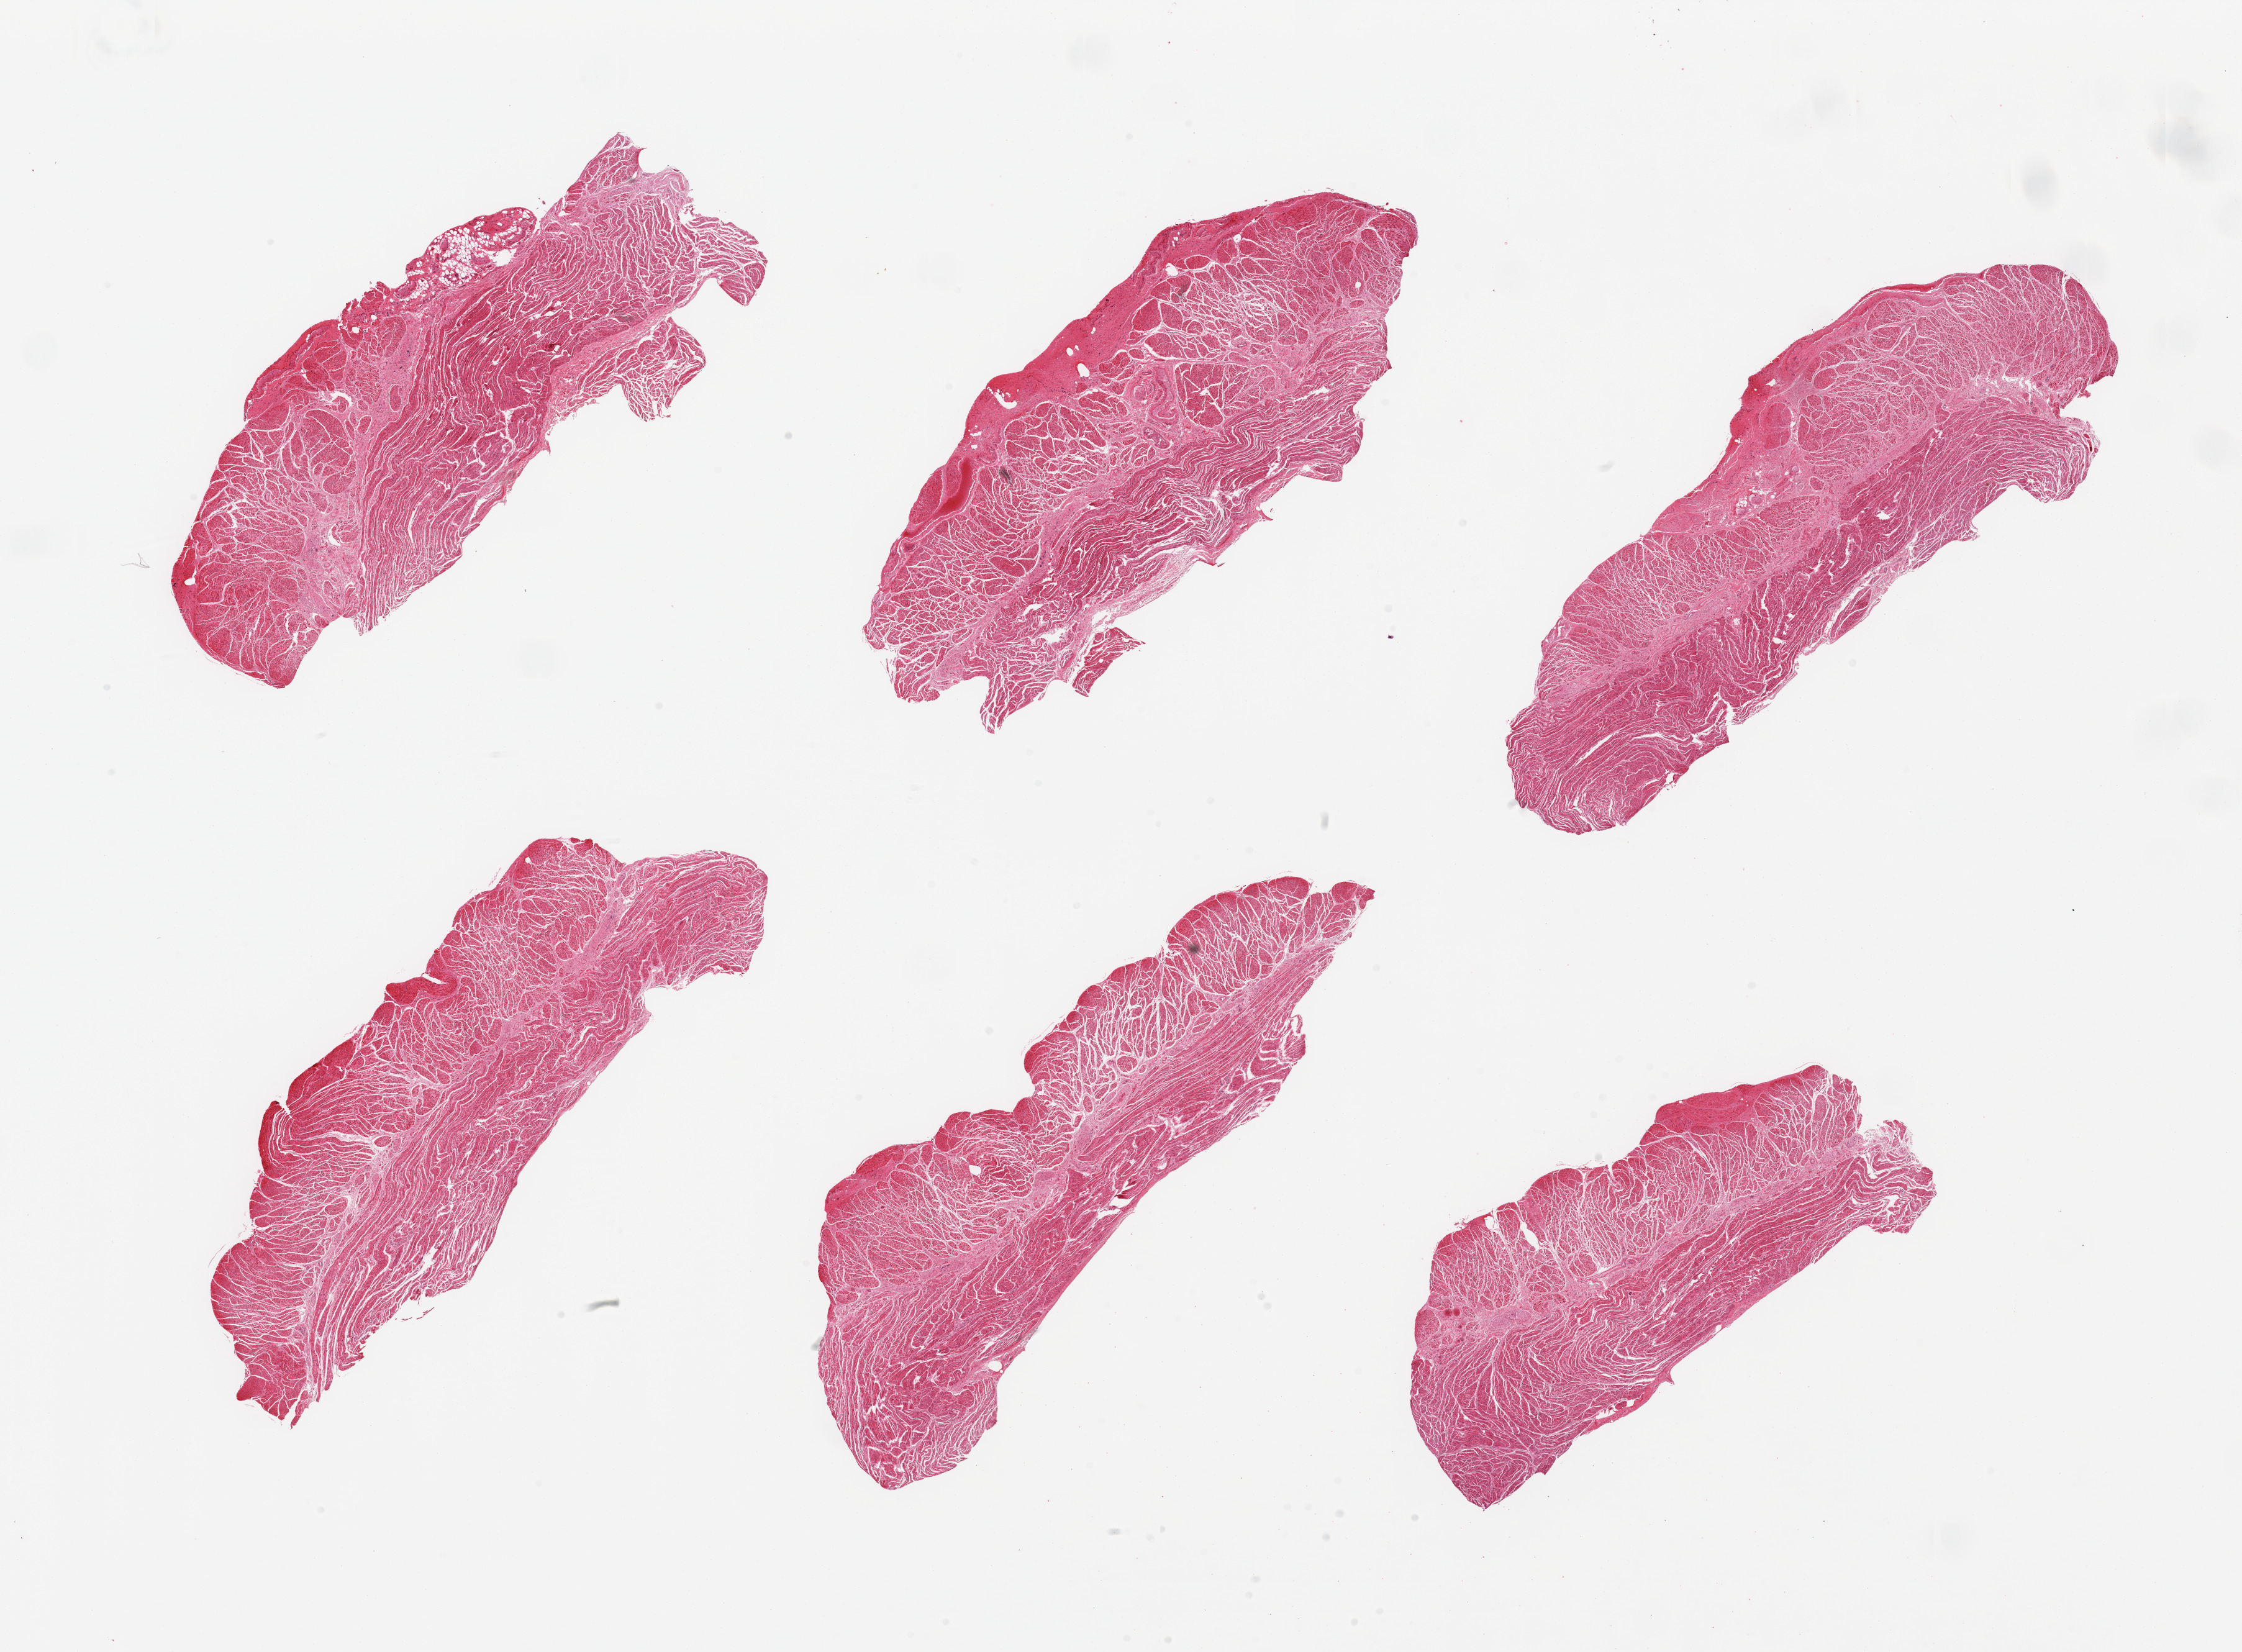
Digitized haematoxylin and eosin-stained section — low-resolution overview of the scanned area, about 28.5 x 21.0 mm (acquisition: 20x scan); PAXgene-fixed, paraffin-embedded tissue; sampled site (target tissue): gastroesophageal junction; donor tissue sample. Donor sex: male.
Review note (as recorded): 6 pieces; target muscularis.